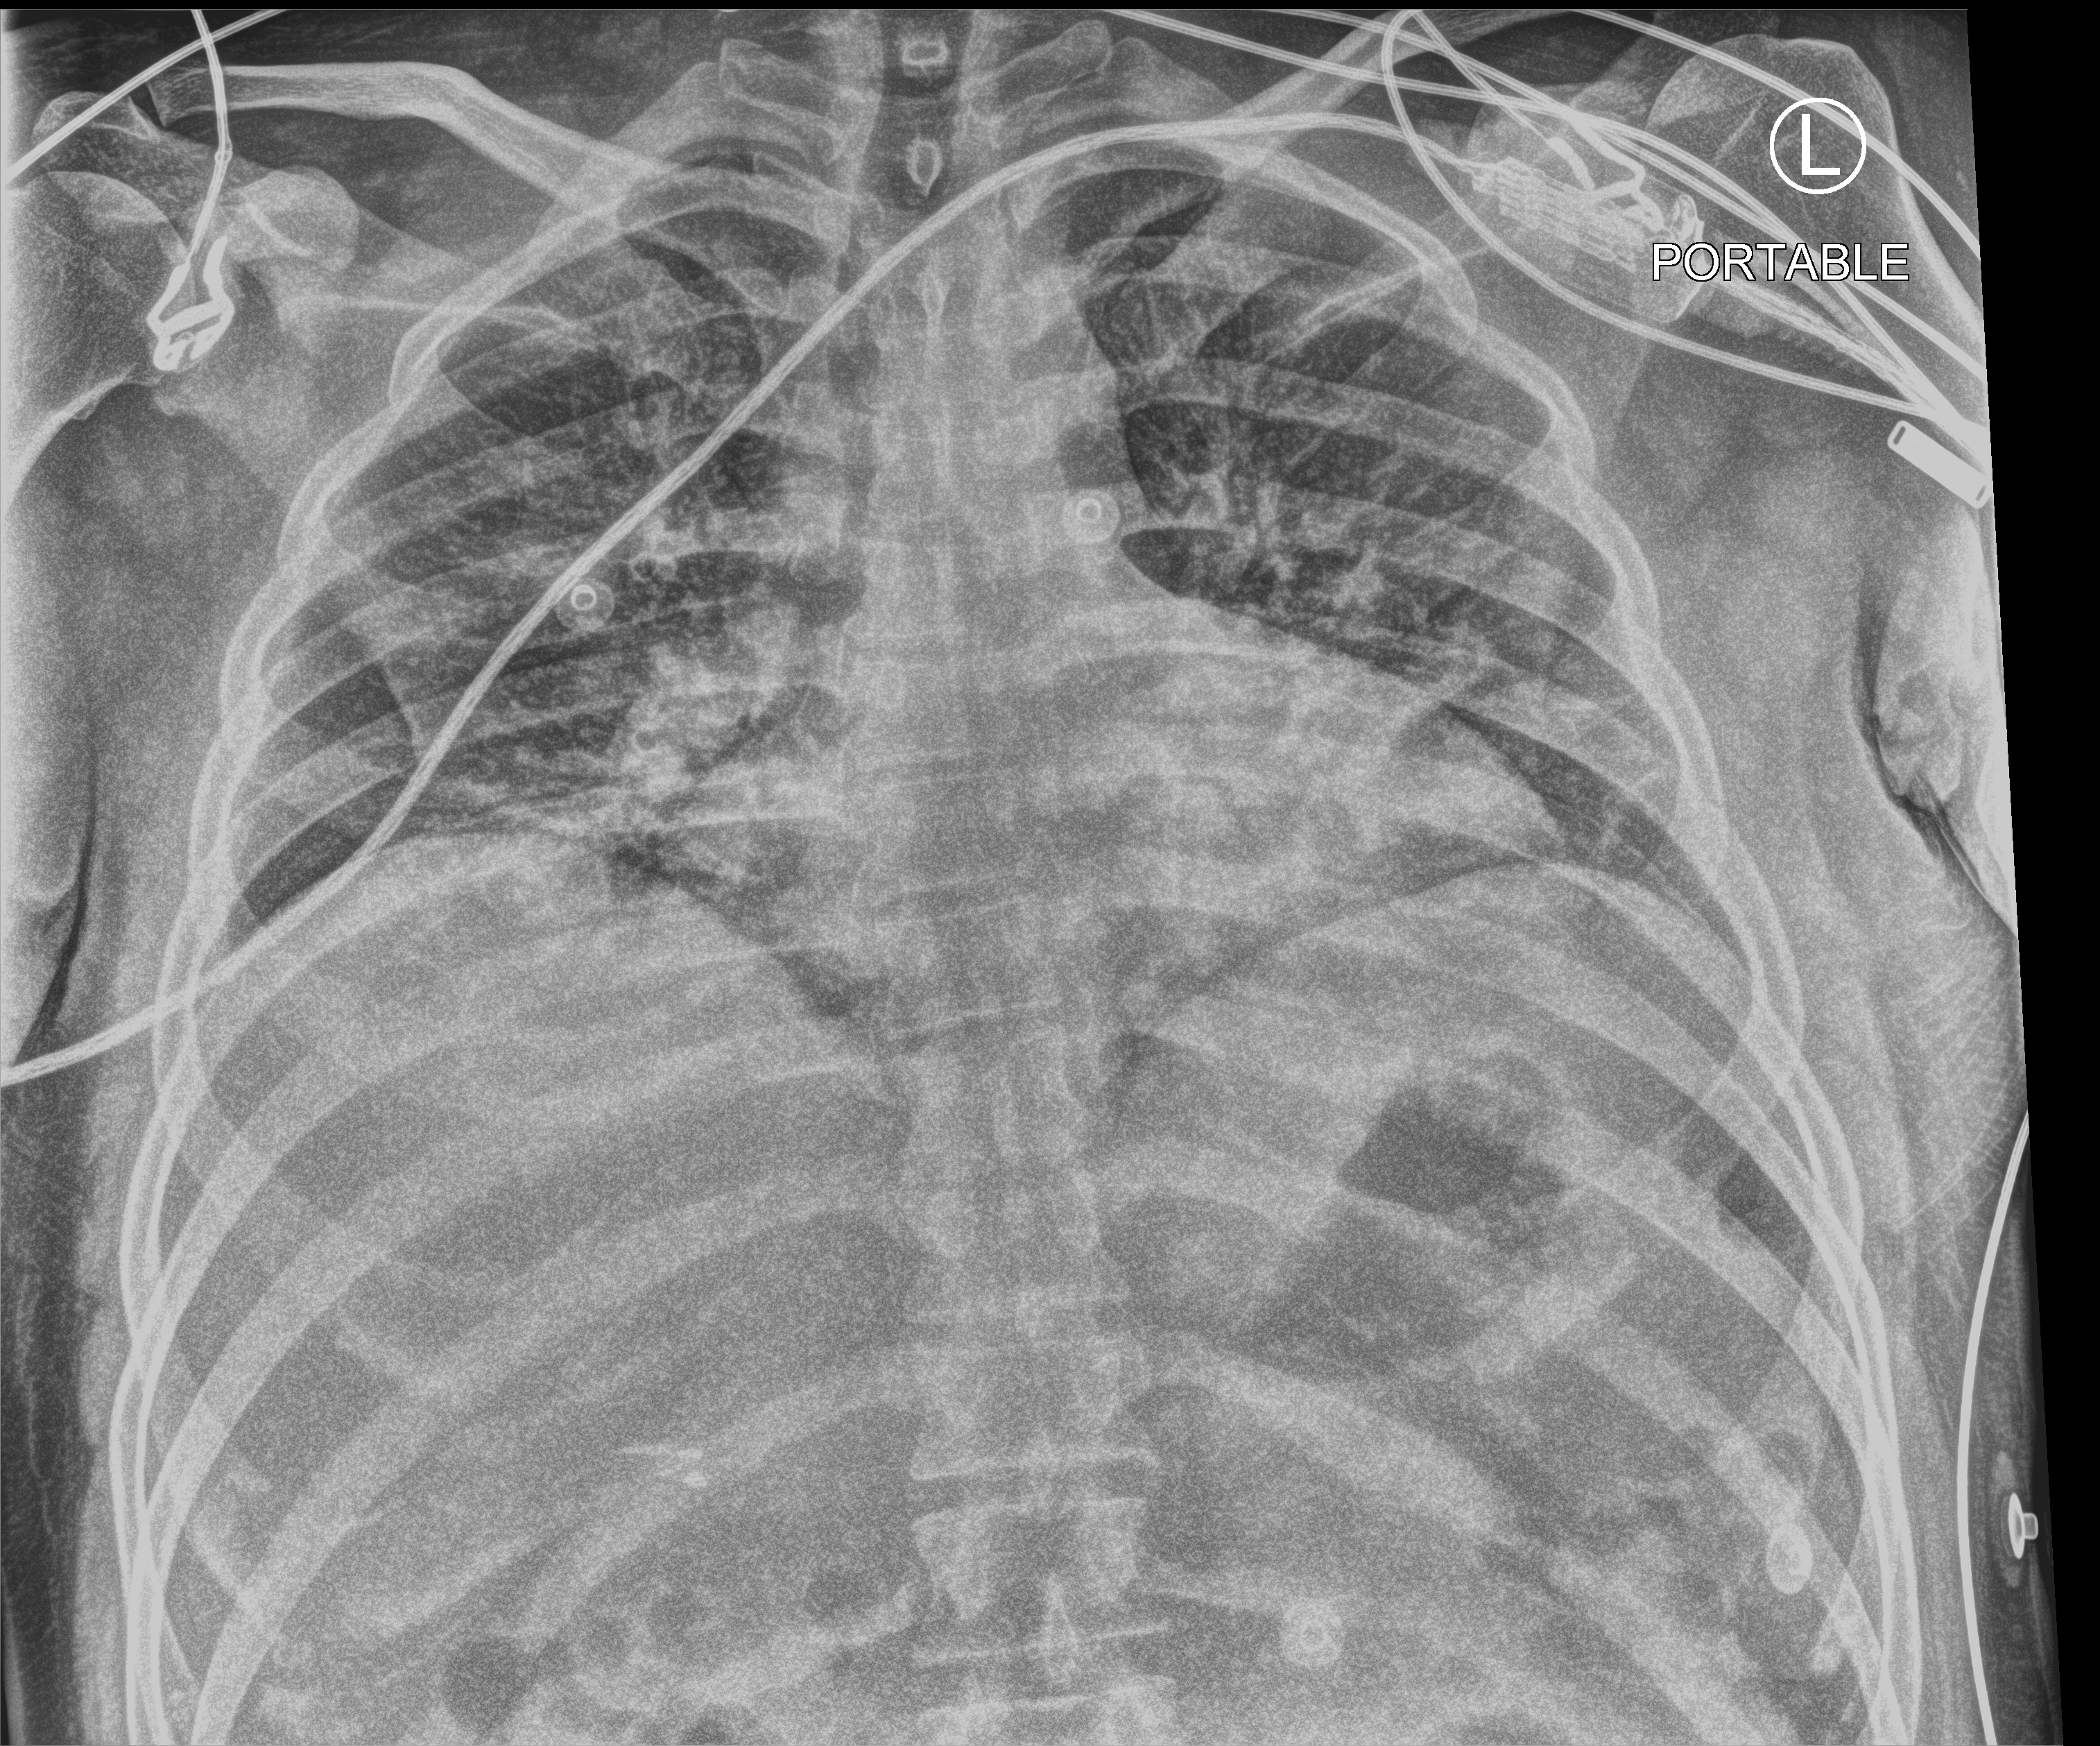
Chest X-ray (portable), anteroposterior (AP) projection. Male patient hospitalised with COVID-19, age 18–59 years.
Hospital-stay facts (about this admission, not read from this image; timing relative to this image not recorded): other chronic lung disease (admission record): no; admitted to intensive care during this hospital stay: no; mechanically ventilated during this hospital stay: no.